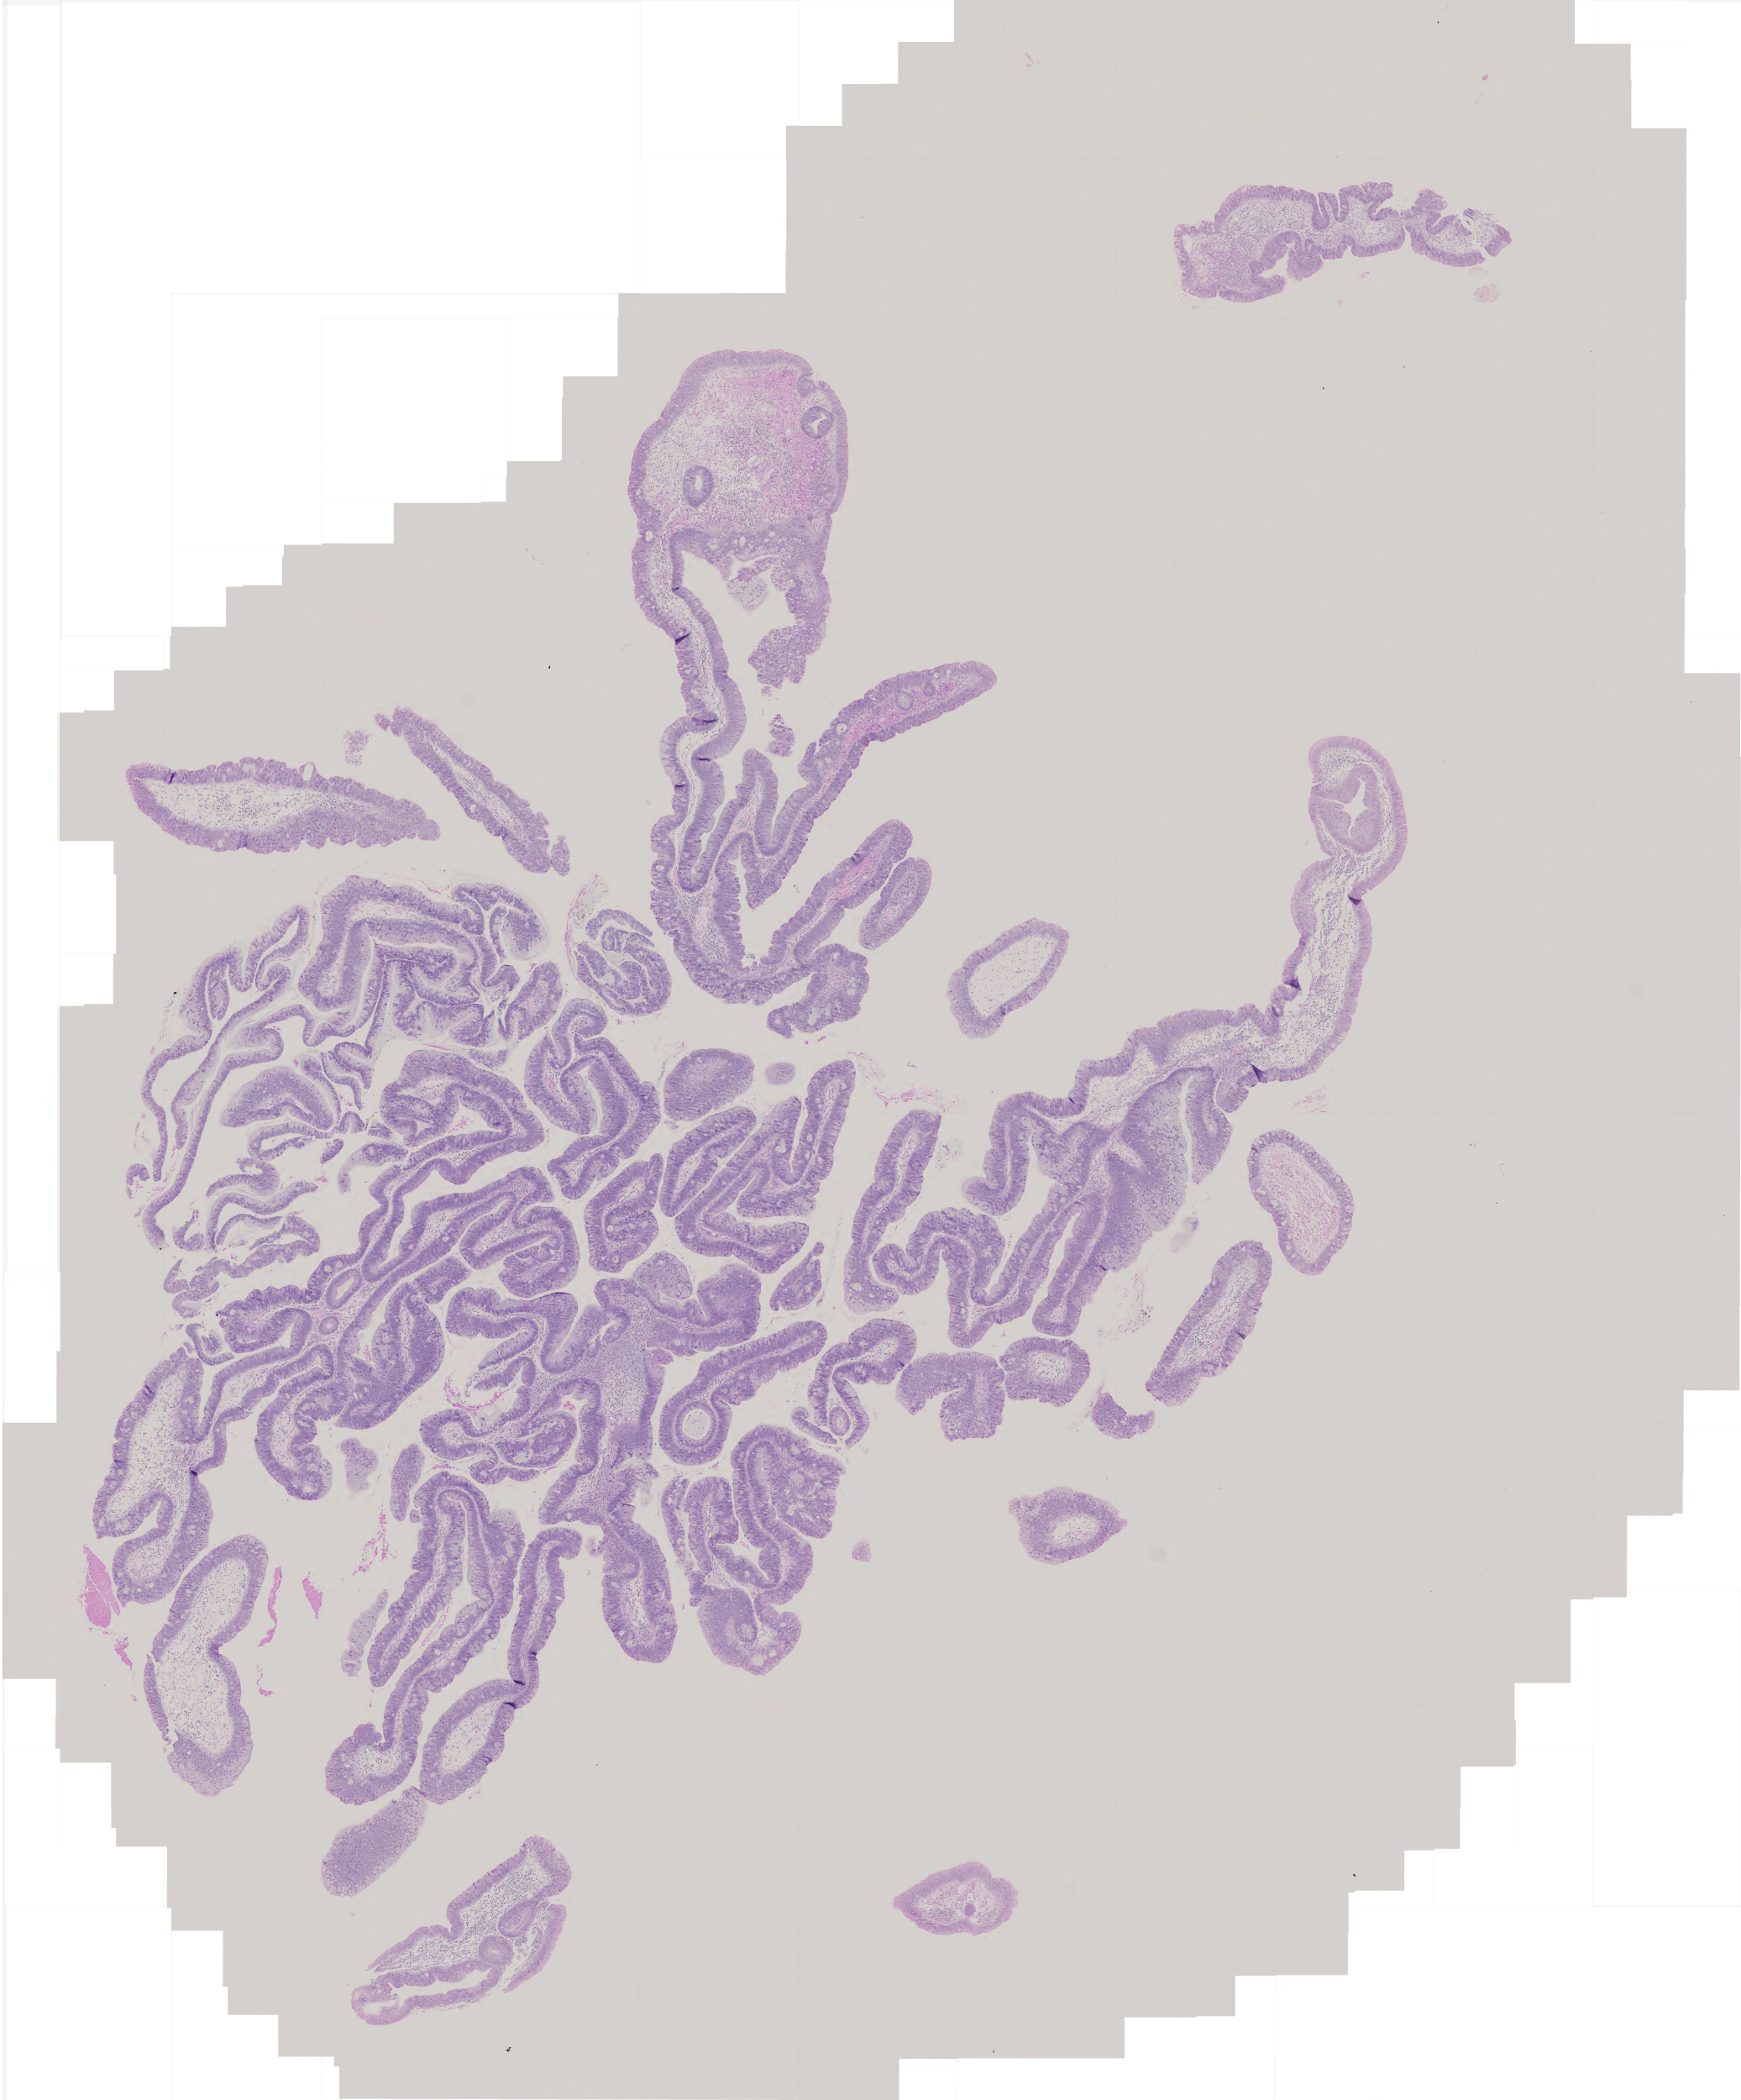
Digitized Hematoxylin and eosin (H&E) stained tissue section (whole slide) — whole scanned area (about 4.1 x 5.0 mm) shown as a low-resolution overview; FFPE section; rectum, primary tumour sample. Female, age 78 years at initial diagnosis.
- AJCC pathologic stage: I (5th edition)
- TNM: T2 N0 M0
- diagnosis: Adenocarcinoma, NOS